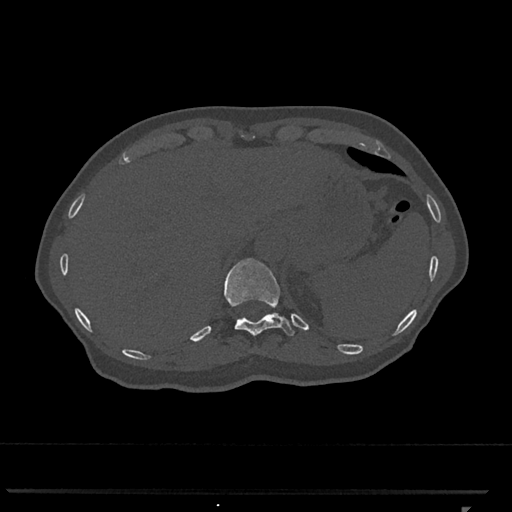
CT including the spine, one axial slice; position 515 of 793 along the scan axis; reconstruction kernel Br40s/3; 120 kVp; bone window (W 1800 / L 400 HU); 0.5 mm slice thickness; 512 × 512 image matrix. Female patient, age 62 years. Case-level facts recorded for this patient, not image findings: primary cancer: renal.
Structures marked on this image (semi-automatic segmentation, software-assisted and operator-edited):
- T11 vertebra: bounding box [x1, y1, x2, y2] px = [224, 258, 294, 336]